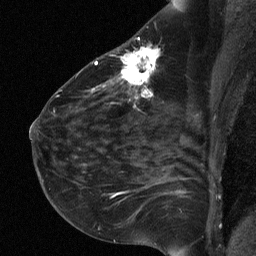
Breast MRI (dynamic contrast-enhanced), one sagittal slice; position 38 of 64 along the scan axis; dynamic contrast-enhanced study with each time point stored as its own series, time point 2 of 3 at this slice position (early post-contrast, ordered by acquisition time); 1.5 T; TE 4.8 ms, TR 27 ms; 2 mm slice thickness; 256 × 256 image matrix, field of view 180 × 180 mm. Female patient, age 51 years. From the clinical record (not read from this slice): setting: breast cancer imaged before/during neoadjuvant chemotherapy; receptor status: HR-positive, HER2-negative.
Structures marked on this image (semi-automatically segmented with operator editing):
- analysis volume of interest (the breast-tissue region the enhancement analysis was run in; not a lesion): bounding box (x1, y1, x2, y2) in pixels: (72, 34, 182, 118)
- tumour enhancement mask (voxels above the 90 % enhancement threshold inside the analysis volume of interest): (92, 47, 160, 107)